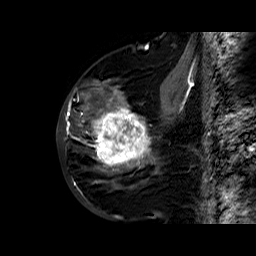
Breast MRI (dynamic contrast-enhanced), one sagittal slice. Slice 23 of 60 in the series (ordered by position). Dynamic contrast-enhanced series, time point 2 of 6 at this slice position (early post-contrast). 1.5 T. TE 6.4 ms, TR 32.8 ms. 4 mm slice thickness. 256 × 256 image matrix, field of view 200 × 200 mm. Female patient. Case-level facts recorded for this patient, not image findings: setting: breast cancer imaged before/during neoadjuvant chemotherapy; receptor status: HR-positive, HER2-negative.
Annotated regions visible in this slice (semi-automatic segmentation, software-assisted and operator-edited):
- analysis volume of interest (the breast-tissue region the enhancement analysis was run in; not a lesion): box from (x=86, y=78) to (x=163, y=177) px
- tumour enhancement mask (voxels above the 100 % enhancement threshold inside the analysis volume of interest): (x=86, y=83)–(x=152, y=171)